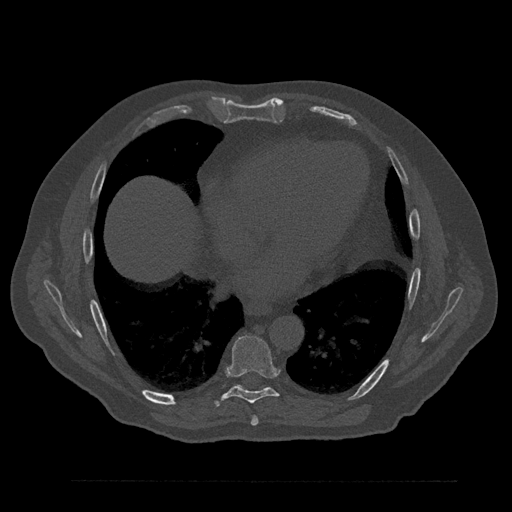
CT including the spine, one axial slice; position 451 of 797 along the scan axis; 120 kVp; bone window (W 1800 / L 400 HU); 512 × 512 image matrix. Male patient, age 61 years. Case-level facts recorded for this patient, not image findings: primary cancer: prostate.
Annotated regions visible in this slice (semi-automatically segmented with operator editing):
- T7 vertebra: bounding box [x1, y1, x2, y2] px = [251, 416, 258, 426]
- T8 vertebra: [213, 335, 279, 407]